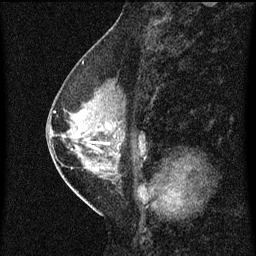
Breast MRI (dynamic contrast-enhanced), one sagittal slice; slice 29 of 60 in the series (ordered by position); dynamic contrast-enhanced series, image 2 of 3 at this slice position (ordered by acquisition); 1.5 T; TE 4.2 ms, TR 8 ms; 2 mm slice thickness; 256 × 256 image matrix. Female patient, age 47 years.
Structures marked on this image (semi-automatic segmentation, software-assisted and operator-edited):
- analysis volume of interest (the breast-tissue region the enhancement analysis was run in; not a lesion): bounding box [x1, y1, x2, y2] px = [54, 80, 144, 187]
- tumour enhancement mask (voxels above the 70 % enhancement threshold inside the analysis volume of interest): [55, 112, 142, 157]